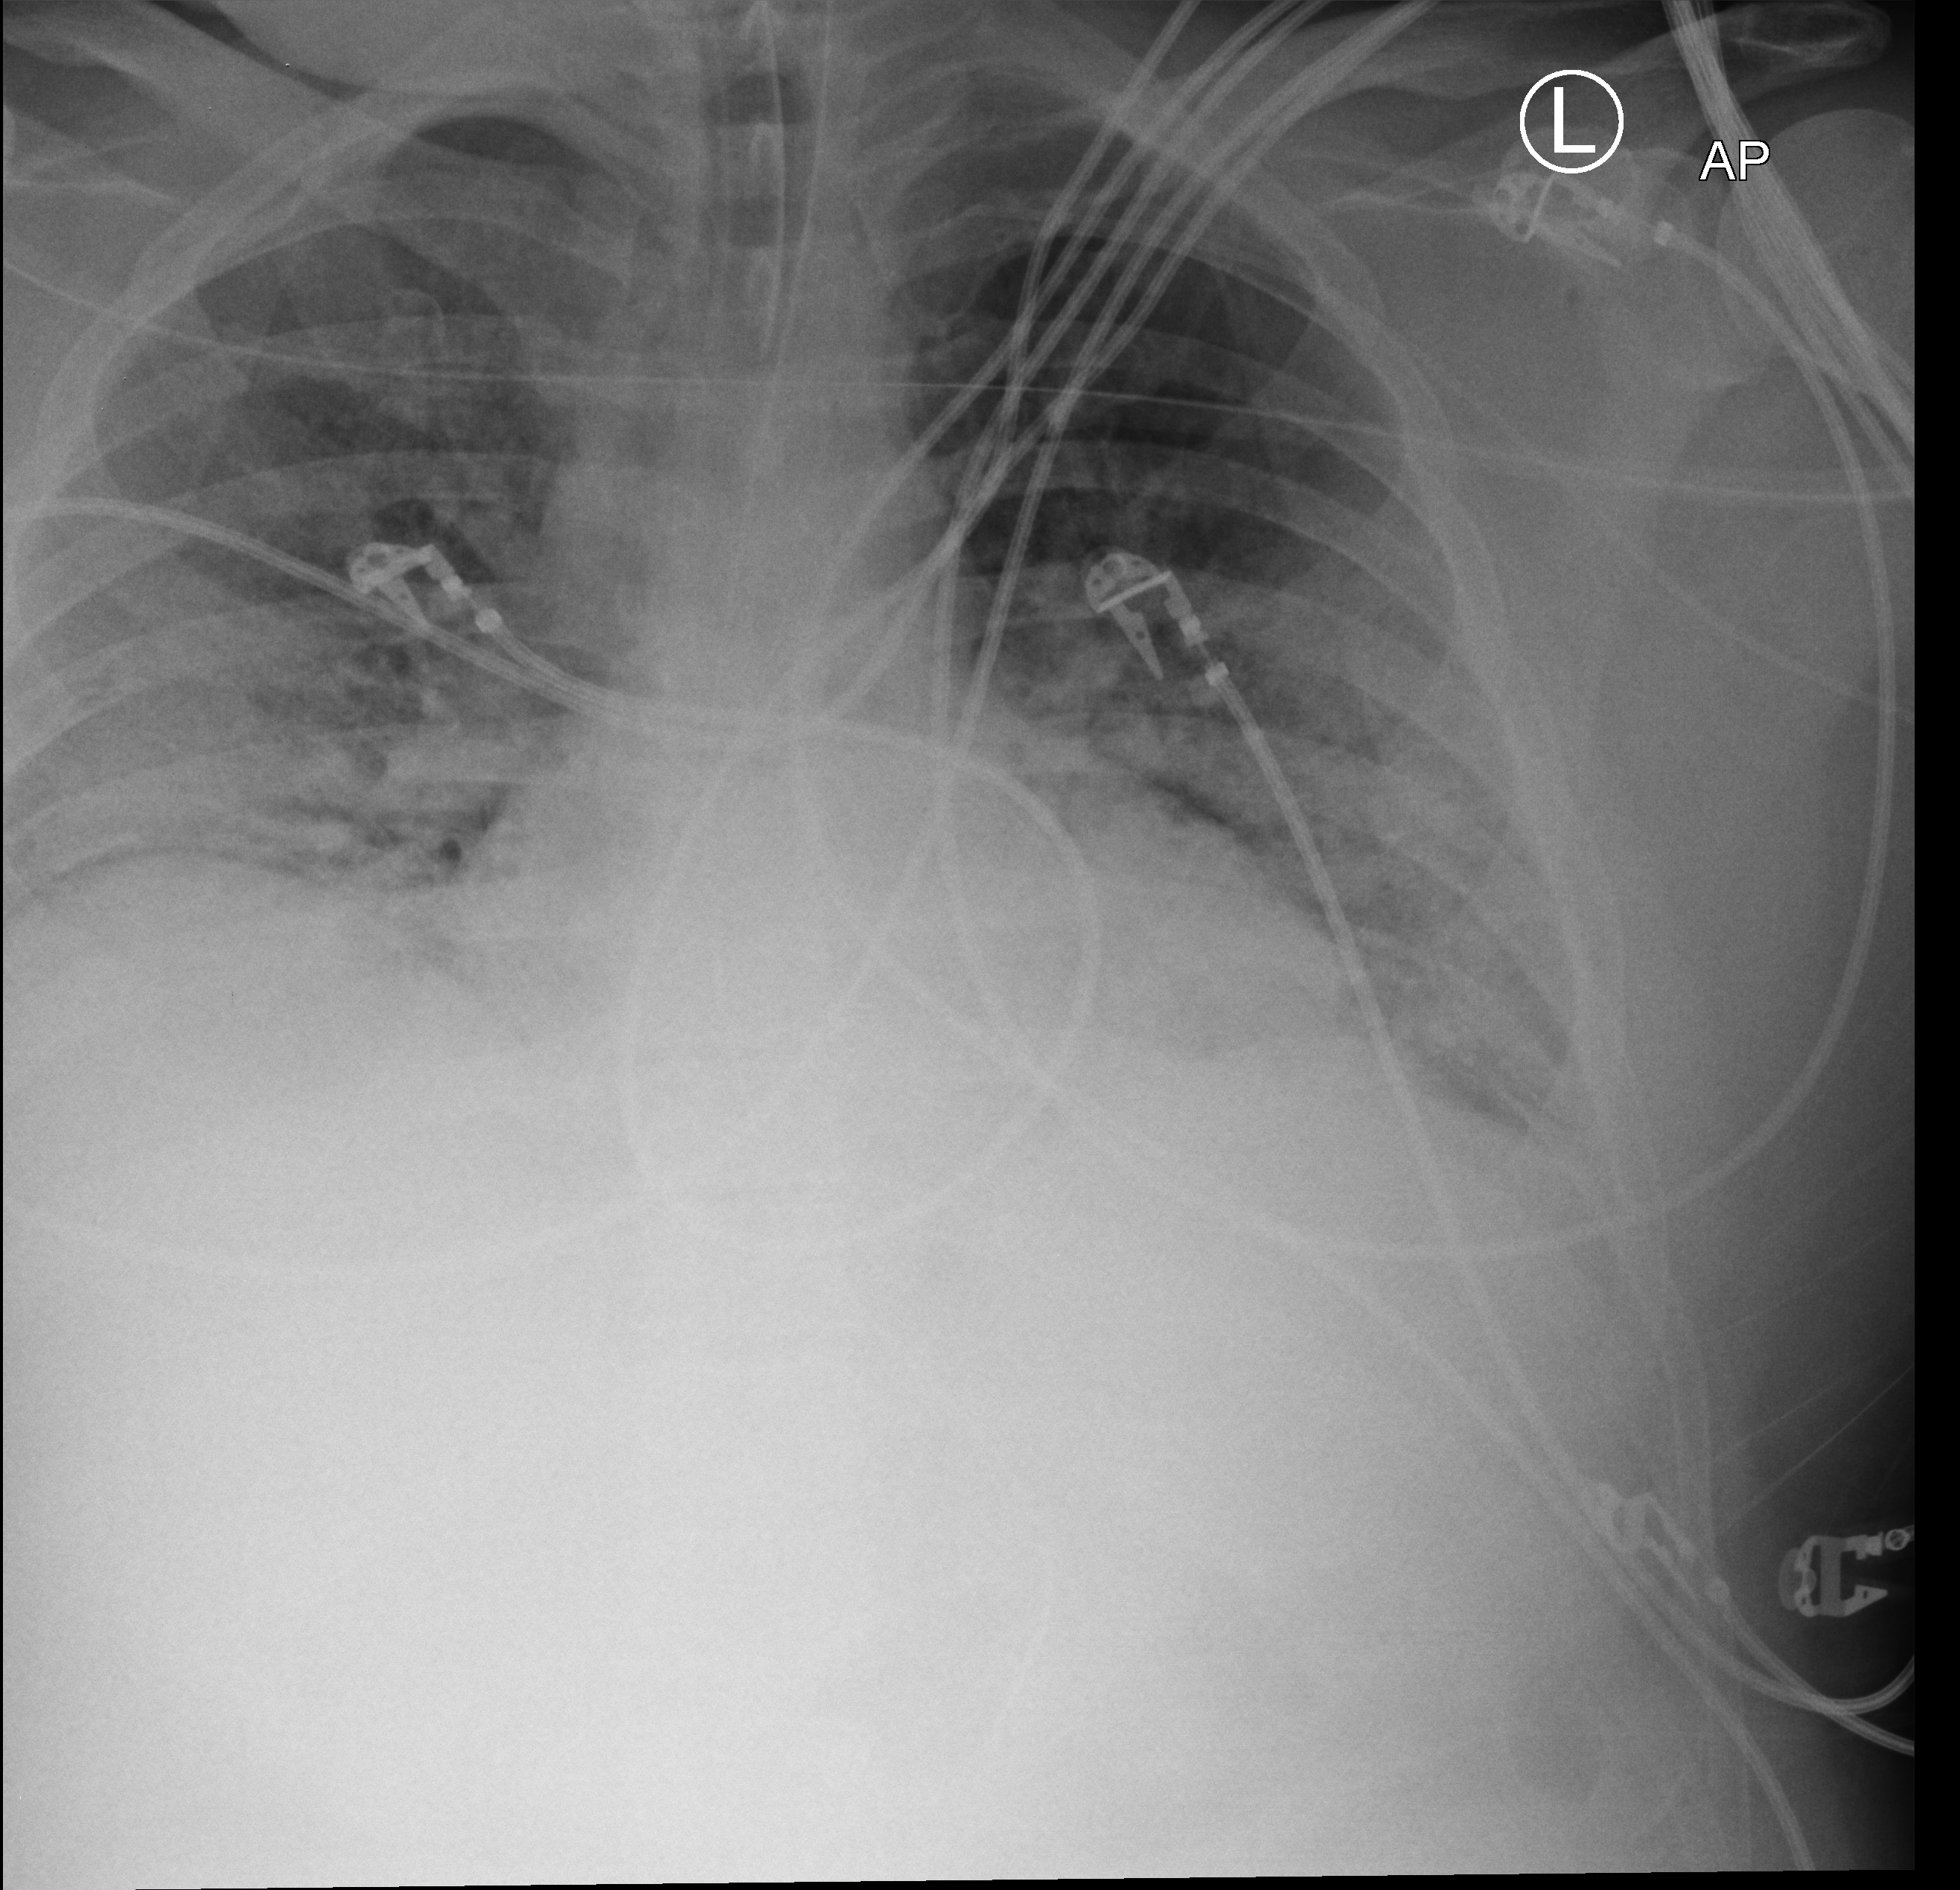
Portable chest radiograph; anteroposterior (AP) projection. Patient hospitalised with COVID-19; male, aged 18–59 years.
From the hospital-stay record, not from the radiograph (when in the stay this image was taken is not recorded): mechanically ventilated during this hospital stay: yes; COPD (admission record): no.